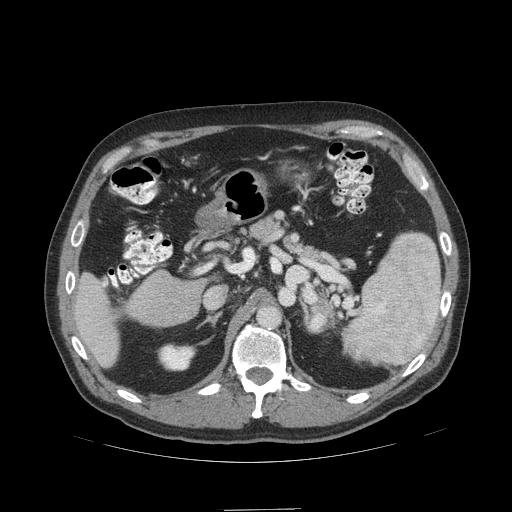
Contrast-enhanced abdominal CT (liver protocol), one axial slice. Position 61 of 99 along the scan axis. Reconstruction kernel STANDARD. Soft-tissue window (W 400 / L 40 HU). 512 × 512 image matrix. Case-level facts recorded for this patient, not image findings: diagnosis: hepatocellular carcinoma (patient treated with transarterial chemoembolisation; whether this scan precedes or follows treatment is not stated here); TNM stage (as recorded): Stage-I; Child-Pugh class: A.
Structures marked on this image (semi-automatic segmentation, software-assisted and operator-edited):
- liver parenchyma outside the tumour (the mass and vessels are separate outlines, so this box may not span the whole liver): bounding box [x1, y1, x2, y2] px = [71, 272, 120, 368]